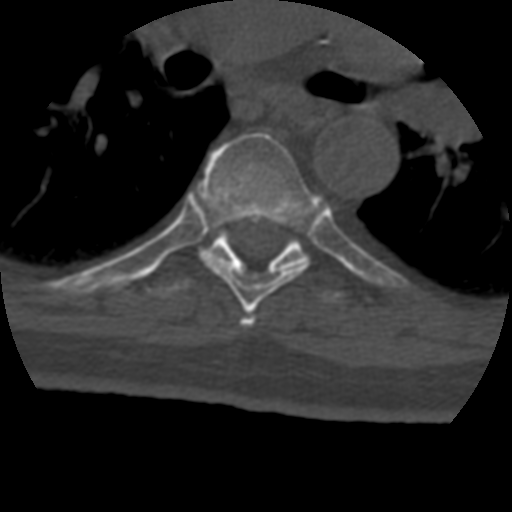
CT including the spine, one axial slice; slice 293 of 399 in the series (ordered by position); reconstruction kernel STANDARD; 120 kVp; bone window (W 1800 / L 400 HU); 512 × 512 image matrix, field of view 160 × 160 mm. Patient age 69 years. Case-level facts recorded for this patient, not image findings: primary cancer: prostate.
Annotated regions visible in this slice (semi-automatically segmented with operator editing):
- T5 vertebra: bounding box [x1, y1, x2, y2] px = [241, 315, 255, 327]
- T6 vertebra: [200, 132, 320, 313]
- T7 vertebra: [147, 228, 352, 304]